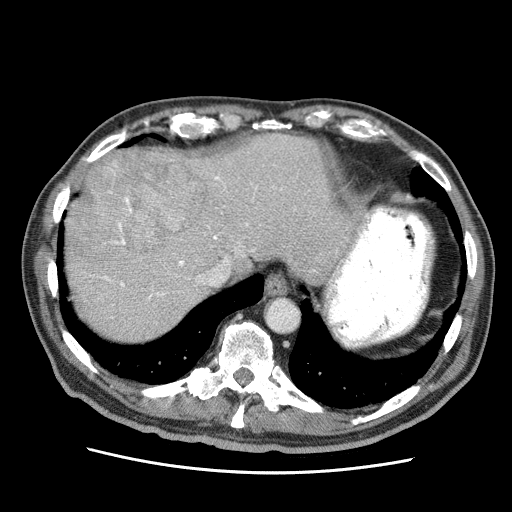
Contrast-enhanced abdominal CT (liver protocol), one axial slice. Slice 54 of 75 in the series (ordered by position). Reconstruction kernel STANDARD. 120 kVp. Soft-tissue window (W 400 / L 40 HU). 512 × 512 image matrix, field of view 360 × 360 mm. From the clinical record (not read from this slice): diagnosis: hepatocellular carcinoma (patient treated with transarterial chemoembolisation; whether this scan precedes or follows treatment is not stated here); TNM stage (as recorded): Stage-IIIA; Child-Pugh class: A; tumour differentiation: well differentiated; tumour nodularity: multinodular.
Outlined on this slice (semi-automatic segmentation, software-assisted and operator-edited):
- abdominal aorta: box from (x=267, y=299) to (x=298, y=331) px
- liver parenchyma outside the tumour (the mass and vessels are separate outlines, so this box may not span the whole liver): (x=64, y=134)–(x=352, y=340)
- mass: (x=68, y=148)–(x=203, y=263)
- liver vessels: (x=103, y=176)–(x=315, y=299)